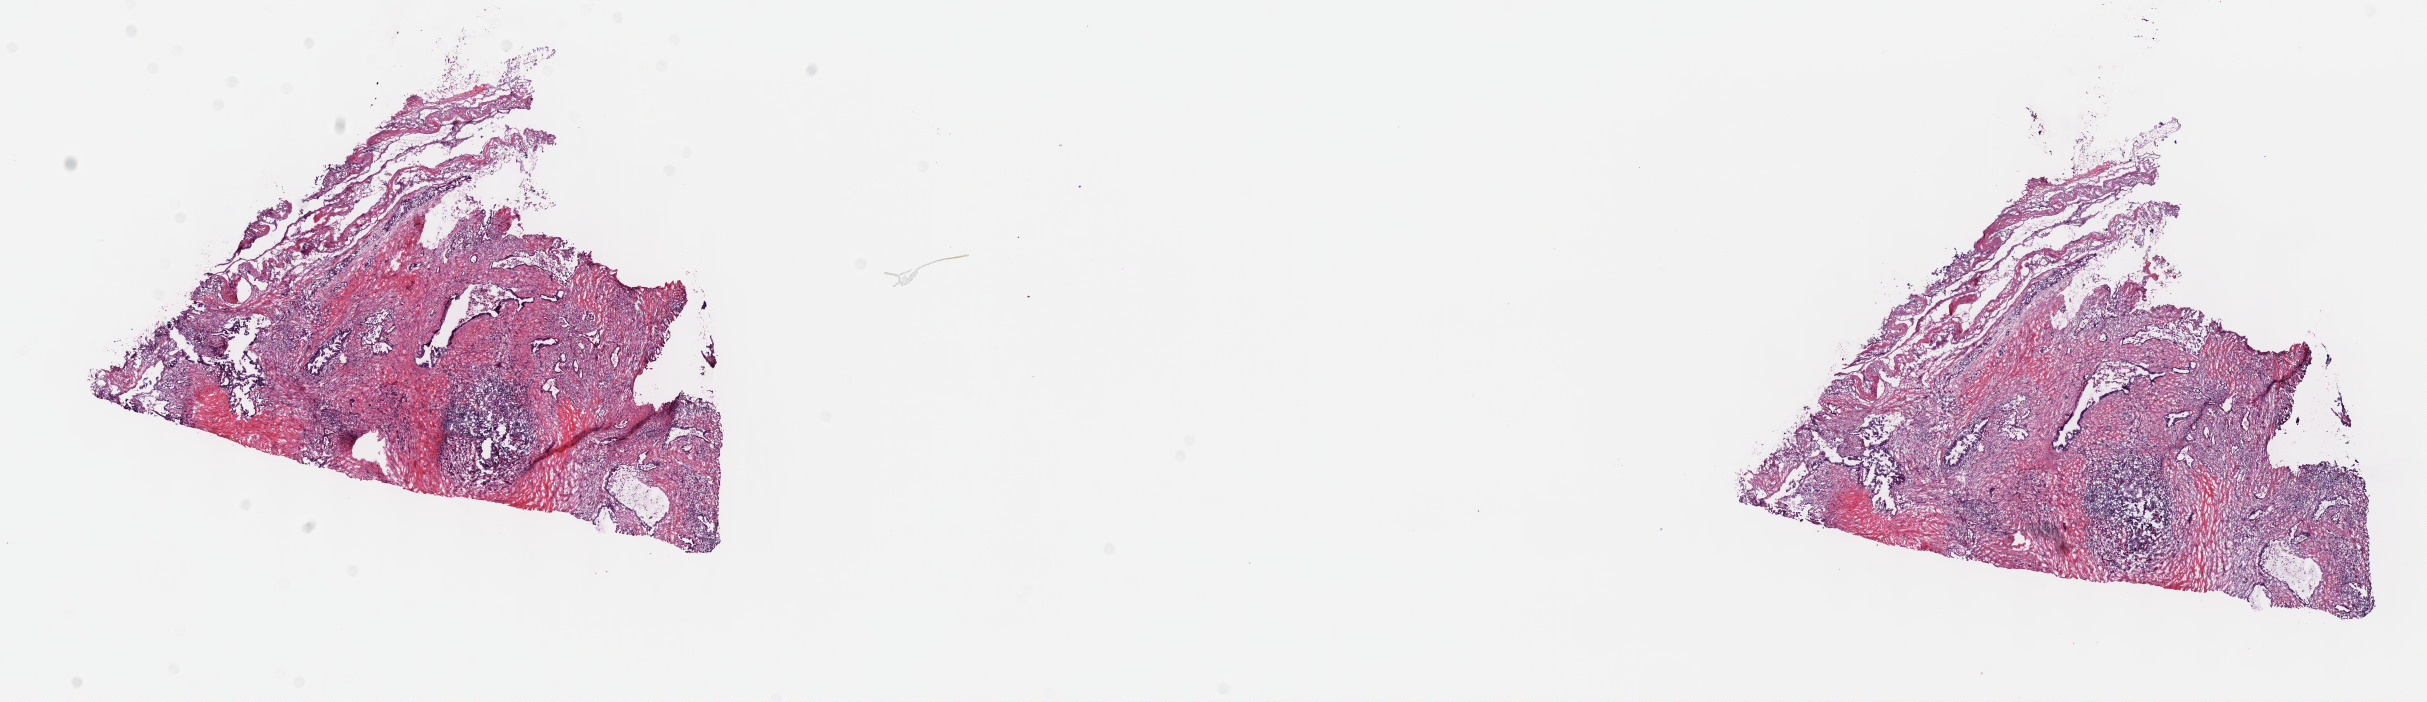
Whole-slide histology image, H&E-stained — low-resolution overview of the scanned area, about 19.6 x 5.7 mm, frozen section from the top of the tissue portion, sample: primary tumour, pancreas. Male patient; age at initial diagnosis 81 years. Histologic grade: G3 (poorly differentiated). Slide review estimates, as recorded: tumour cells 30%, tumour nuclei 75%, normal cells 0%, stromal cells 65%, necrosis 5%. Infiltration values recorded for this section: lymphocyte infiltration 15%, monocyte infiltration 2%, neutrophil infiltration 2%.
• TNM: T3 N1 MX
• diagnosis: Infiltrating duct carcinoma, NOS (body of pancreas)
• AJCC pathologic stage: IIB (7th edition)